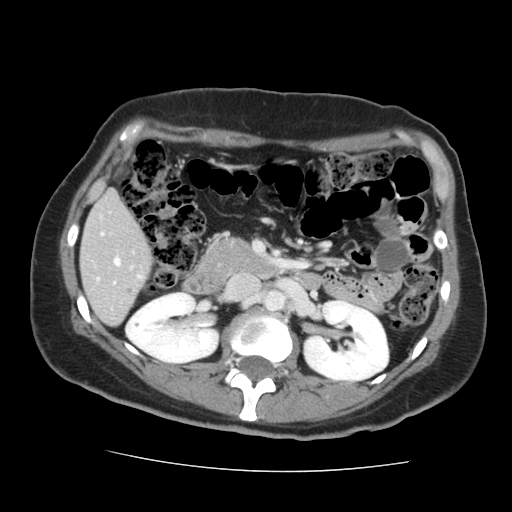
Contrast-enhanced abdominal CT, one axial slice; slice 65 of 144 in the series (ordered by position); 120 kVp; intravenous contrast given; soft-tissue window (W 400 / L 40 HU); 2.5 mm slice thickness; 512 × 512 image matrix, field of view 333 × 333 mm. Female patient, age 46 years. Case-level facts recorded for this patient, not image findings: diagnosis: colorectal cancer liver metastases, imaged before liver resection; multiple liver metastases: no; largest metastasis: 2.8 cm; chemotherapy before resection: yes.
Annotated regions visible in this slice (expert manual segmentation):
- liver: bounding box (x1, y1, x2, y2) in pixels: (81, 193, 150, 325)
- planned liver remnant (the part of the liver to remain after resection): (81, 193, 150, 325)
- portal vein (with intrahepatic branches): (97, 233, 119, 284)